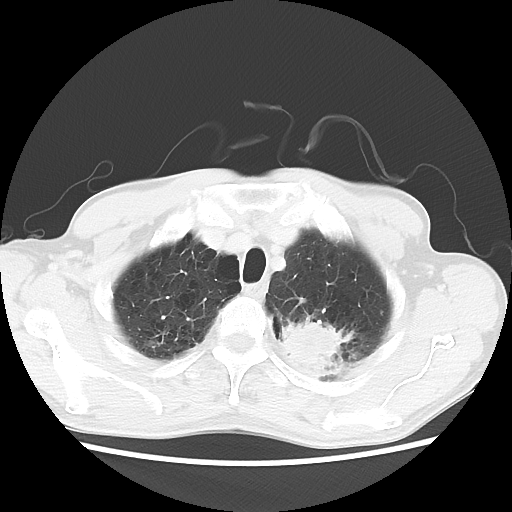
Chest CT, one axial slice; position 55 of 64 along the scan axis; reconstruction kernel LUNG; 120 kVp; lung window (W 1500 / L -600 HU); 5 mm slice thickness; 512 × 512 image matrix. Patient: male, 63 years. Case-level facts recorded for this patient, not image findings: clinical TNM (as recorded): T2 N0 M0.
Outlined on this slice (bounding box drawn by a radiologist):
- lung tumour (recorded histology: adenocarcinoma): bounding box (x1, y1, x2, y2) in pixels: (277, 309, 356, 392)